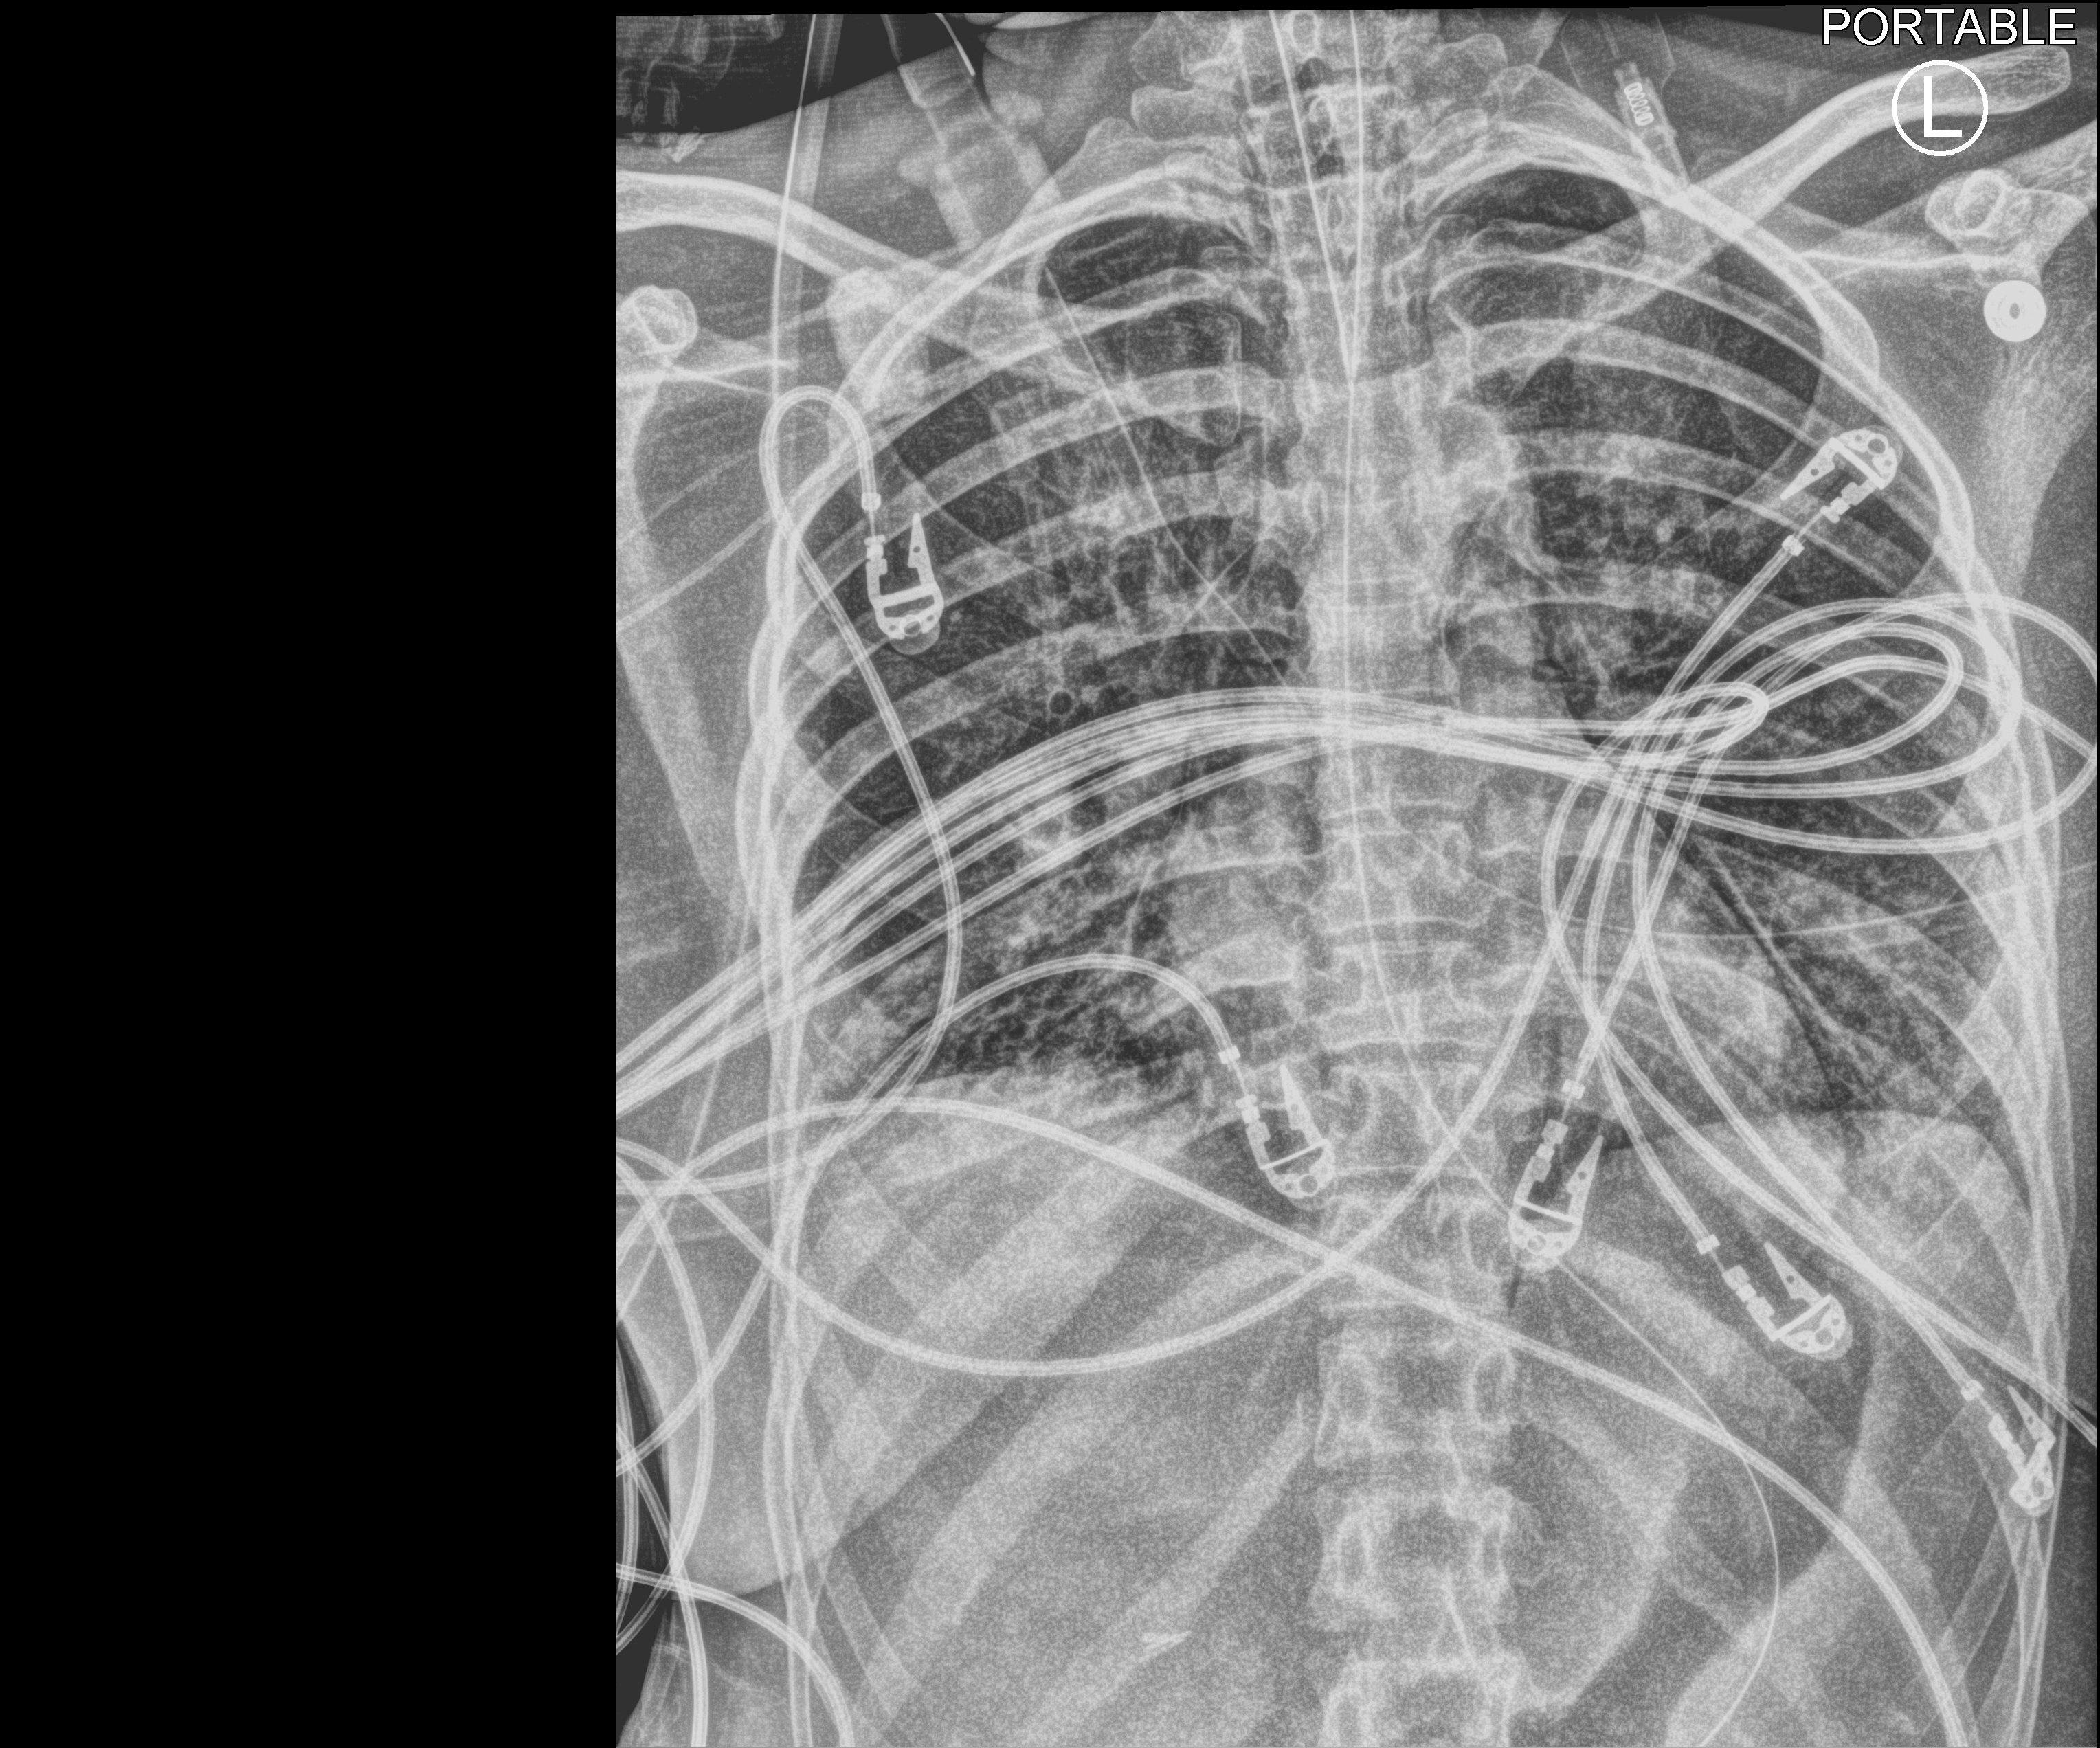
Portable chest radiograph, anteroposterior (AP) projection. Patient hospitalised with COVID-19, aged 18–59 years.
Admission-level facts for this patient (not findings on this image; timing relative to this image not recorded):
- admitted to intensive care during this hospital stay: yes
- COPD (admission record): no
- hypertension (admission record): no